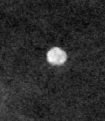
Region of interest cut from a scanned film mammogram (one marked finding), left breast, CC view.
Calcifications, morphology lucent centered; BI-RADS assessment category 2; subtlety rating 3 on a 1 (subtle) to 5 (obvious) scale; benign; no additional work-up was recommended (benign without callback).